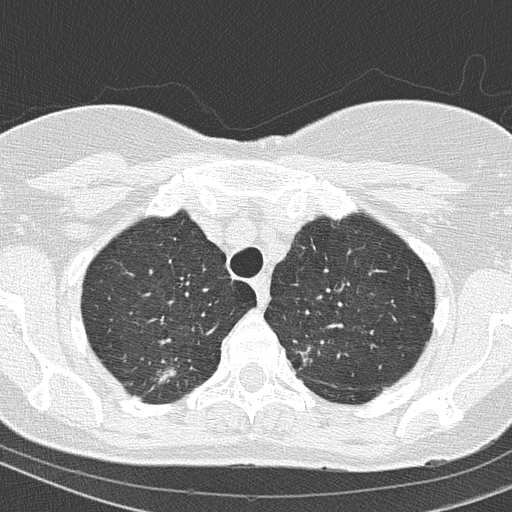
Low-dose screening chest CT, one axial slice. Slice 127 of 154 in the series (ordered by position). 120 kVp. Lung window (W 1500 / L -600 HU). 512 × 512 image matrix, field of view 288 × 288 mm.
Structures marked on this image (expert manual segmentation):
- lesion 1 (tumor, upper lobe of right lung): bounding box <155,366,176,384> (left, top, right, bottom; pixels)